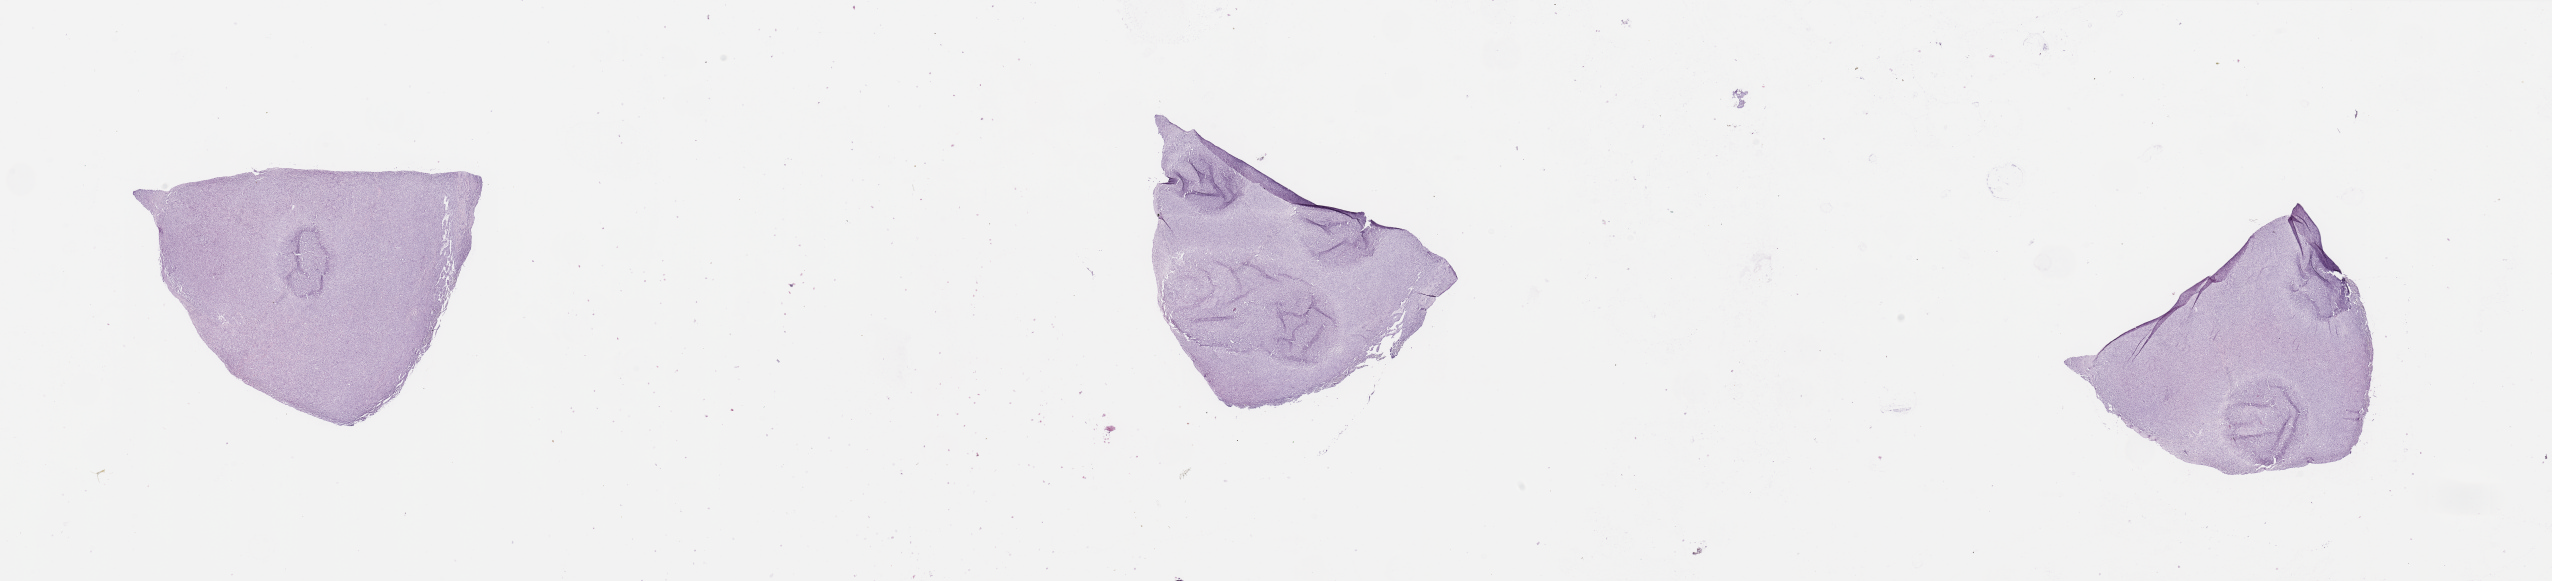
Whole-slide histology image, H&E — shown as a low-resolution overview of the whole scanned area (about 40.4 x 9.2 mm); tumour tissue sample, sampled site: lung. 51-year-old male patient. Histologic grade: G2 (moderately differentiated). Pathologist review of this section (percent, as recorded): tumour nuclei 85%, necrosis 3%.
• primary tumour site (as recorded): right middle lobe
• AJCC pathologic stage: IIB
• diagnosis: Squamous cell carcinoma, NOS